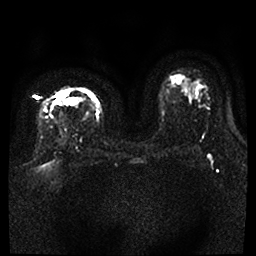
Breast MRI, one axial slice. Diffusion-weighted series; image 2 of 4 stored at this slice position (different b-values; order by instance number). 1.5 T. 256 × 256 image matrix, field of view 360 × 360 mm. Female patient.
Annotated regions visible in this slice (expert manual segmentation):
- tumour on diffusion-weighted imaging: bounding box [x1, y1, x2, y2] px = [56, 91, 77, 105]